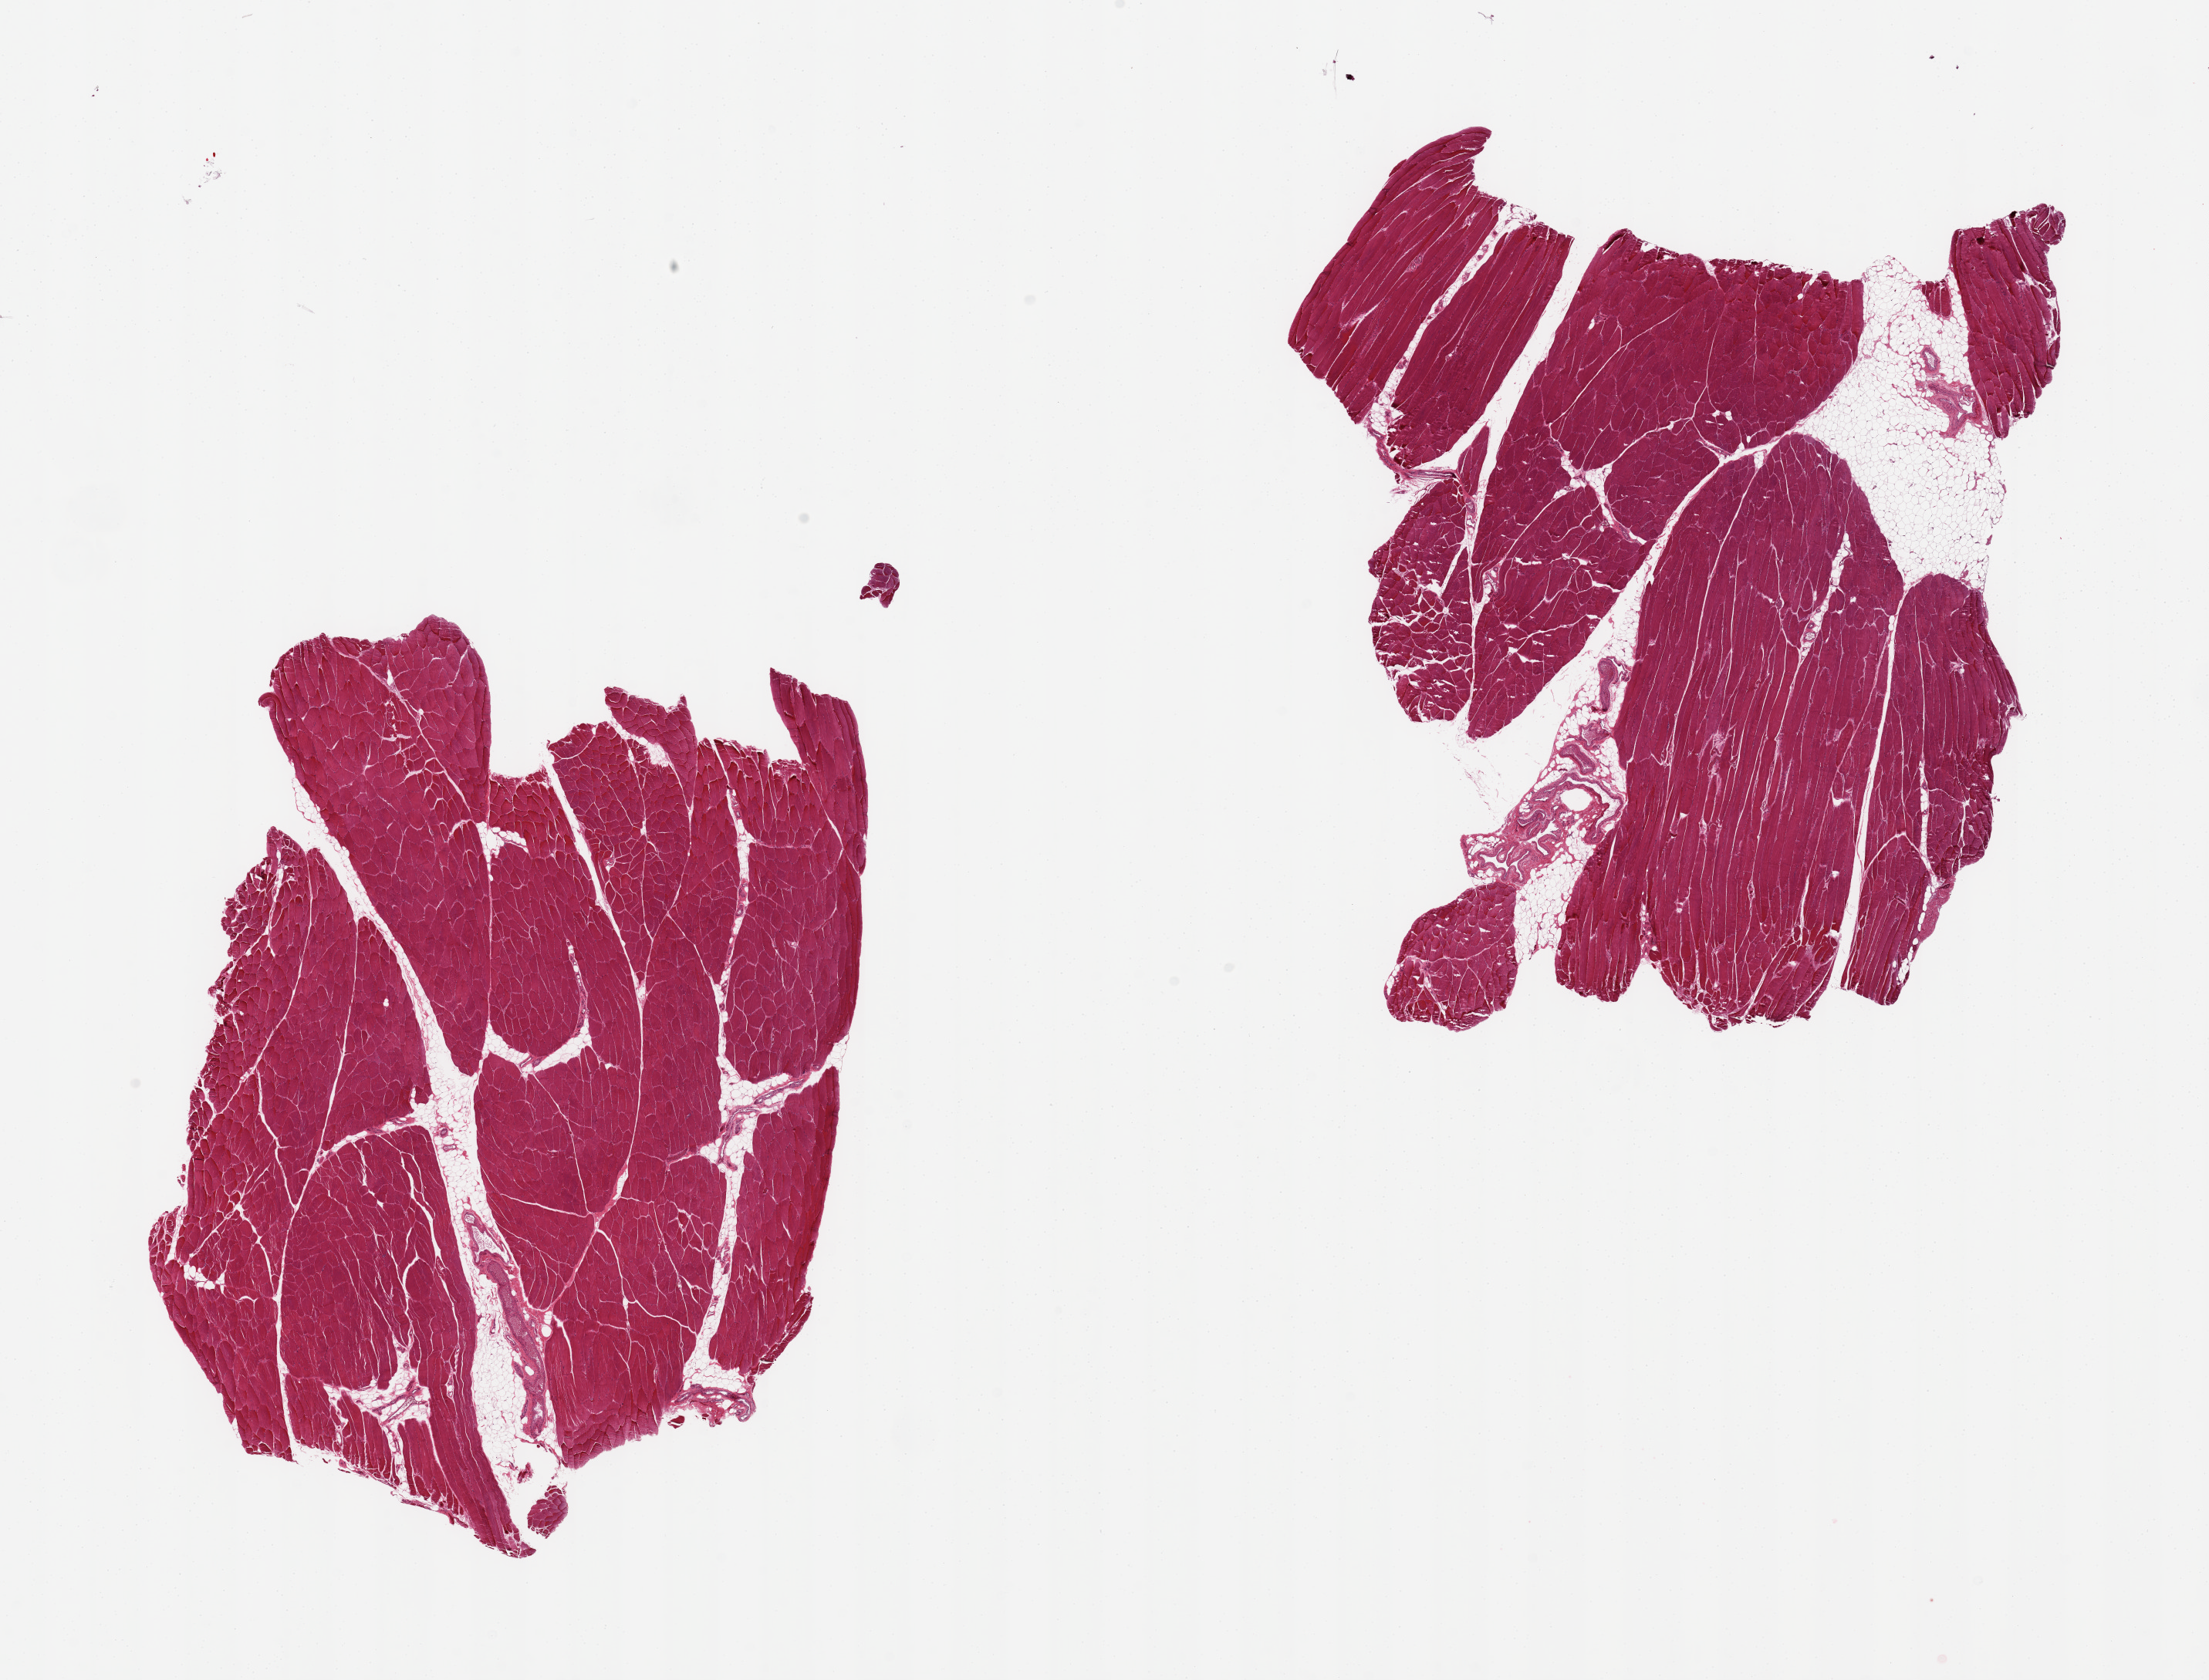
Digitized H&E-stained section, low-resolution overview of the scanned area, about 22.6 x 17.2 mm (from a 20x scan), PAXgene-fixed, paraffin-embedded tissue, section of skeletal muscle (target tissue), tissue donor sample. Donor sex: male.
Pathologist's review note for this sample: 2 pieces, includes ~10% fat and vascular tissue.